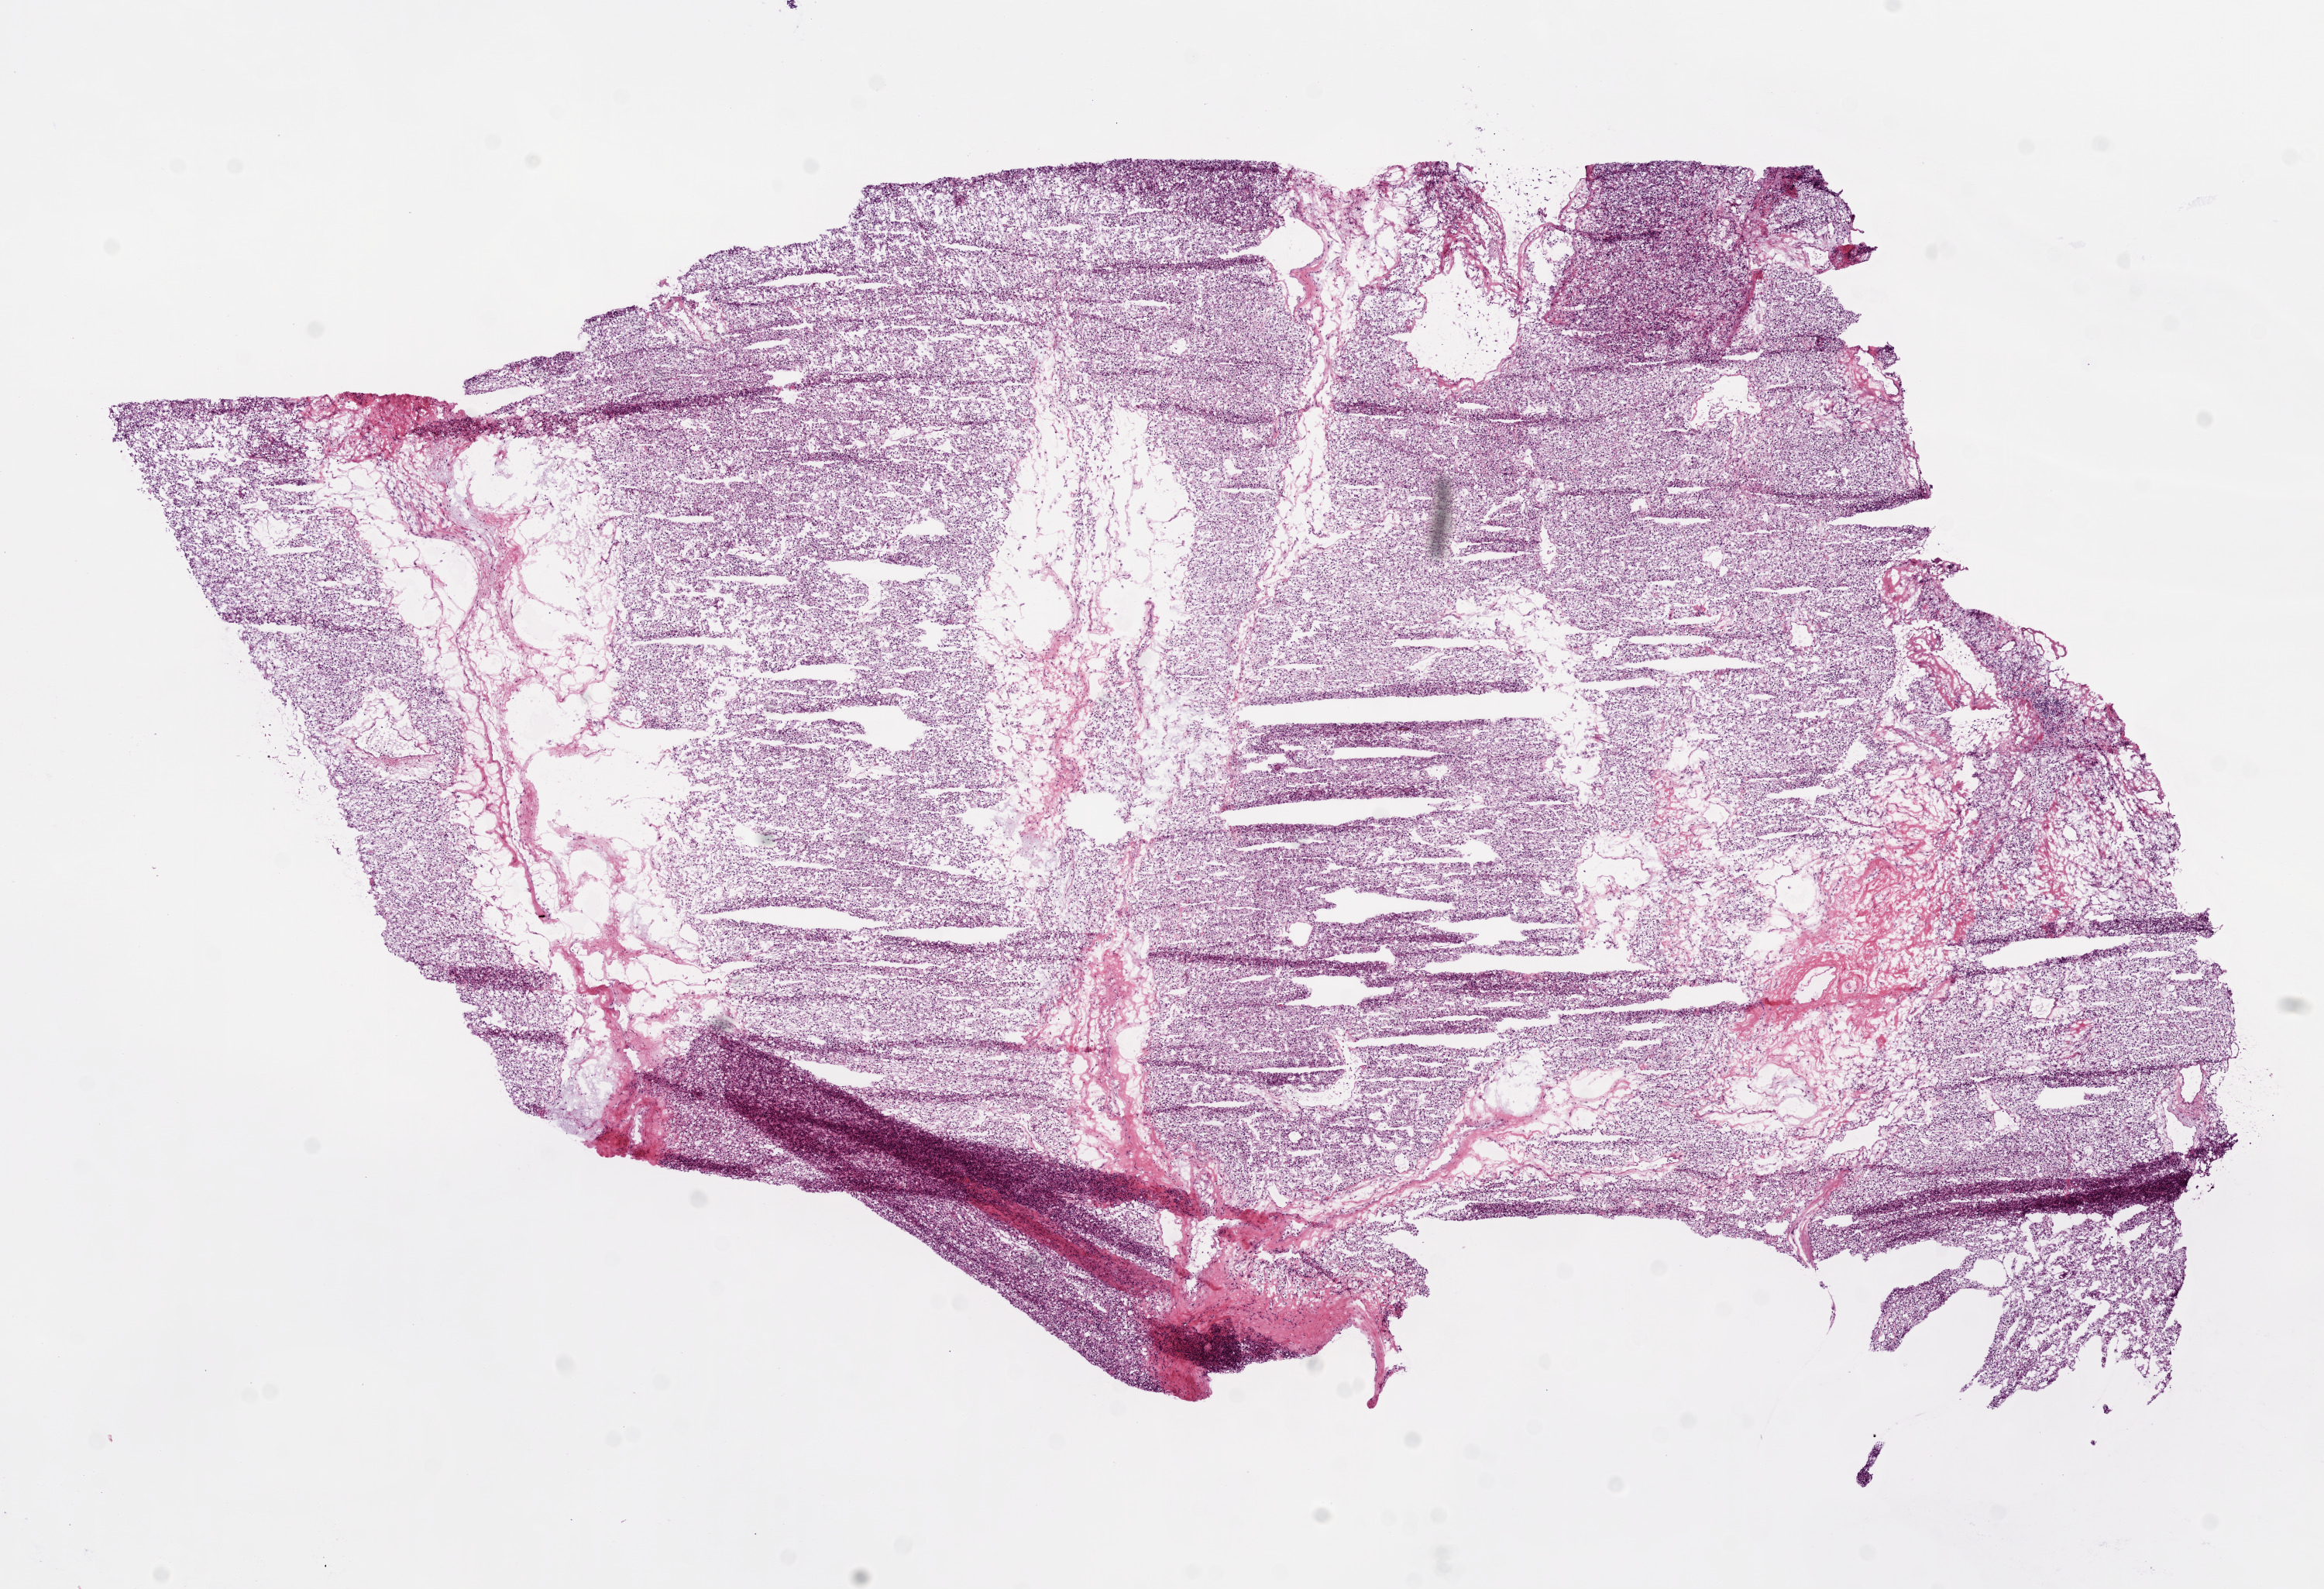
Digitized H&E tissue section (whole slide), low-resolution overview of the scanned area, about 12.0 x 8.2 mm (slide scanned at 20x), frozen section from the bottom of the tissue portion, primary tumour sample from the kidney. Patient sex: female. Histologic grade: G2 (moderately differentiated). Composition of this section per pathologist review: tumour cells 90%, tumour nuclei 85%, normal cells 0%, stromal cells 10%, necrosis 0%.
- TNM: T1 N0 M0
- AJCC pathologic stage: I
- laterality: right
- pathologic diagnosis: Clear cell adenocarcinoma, NOS